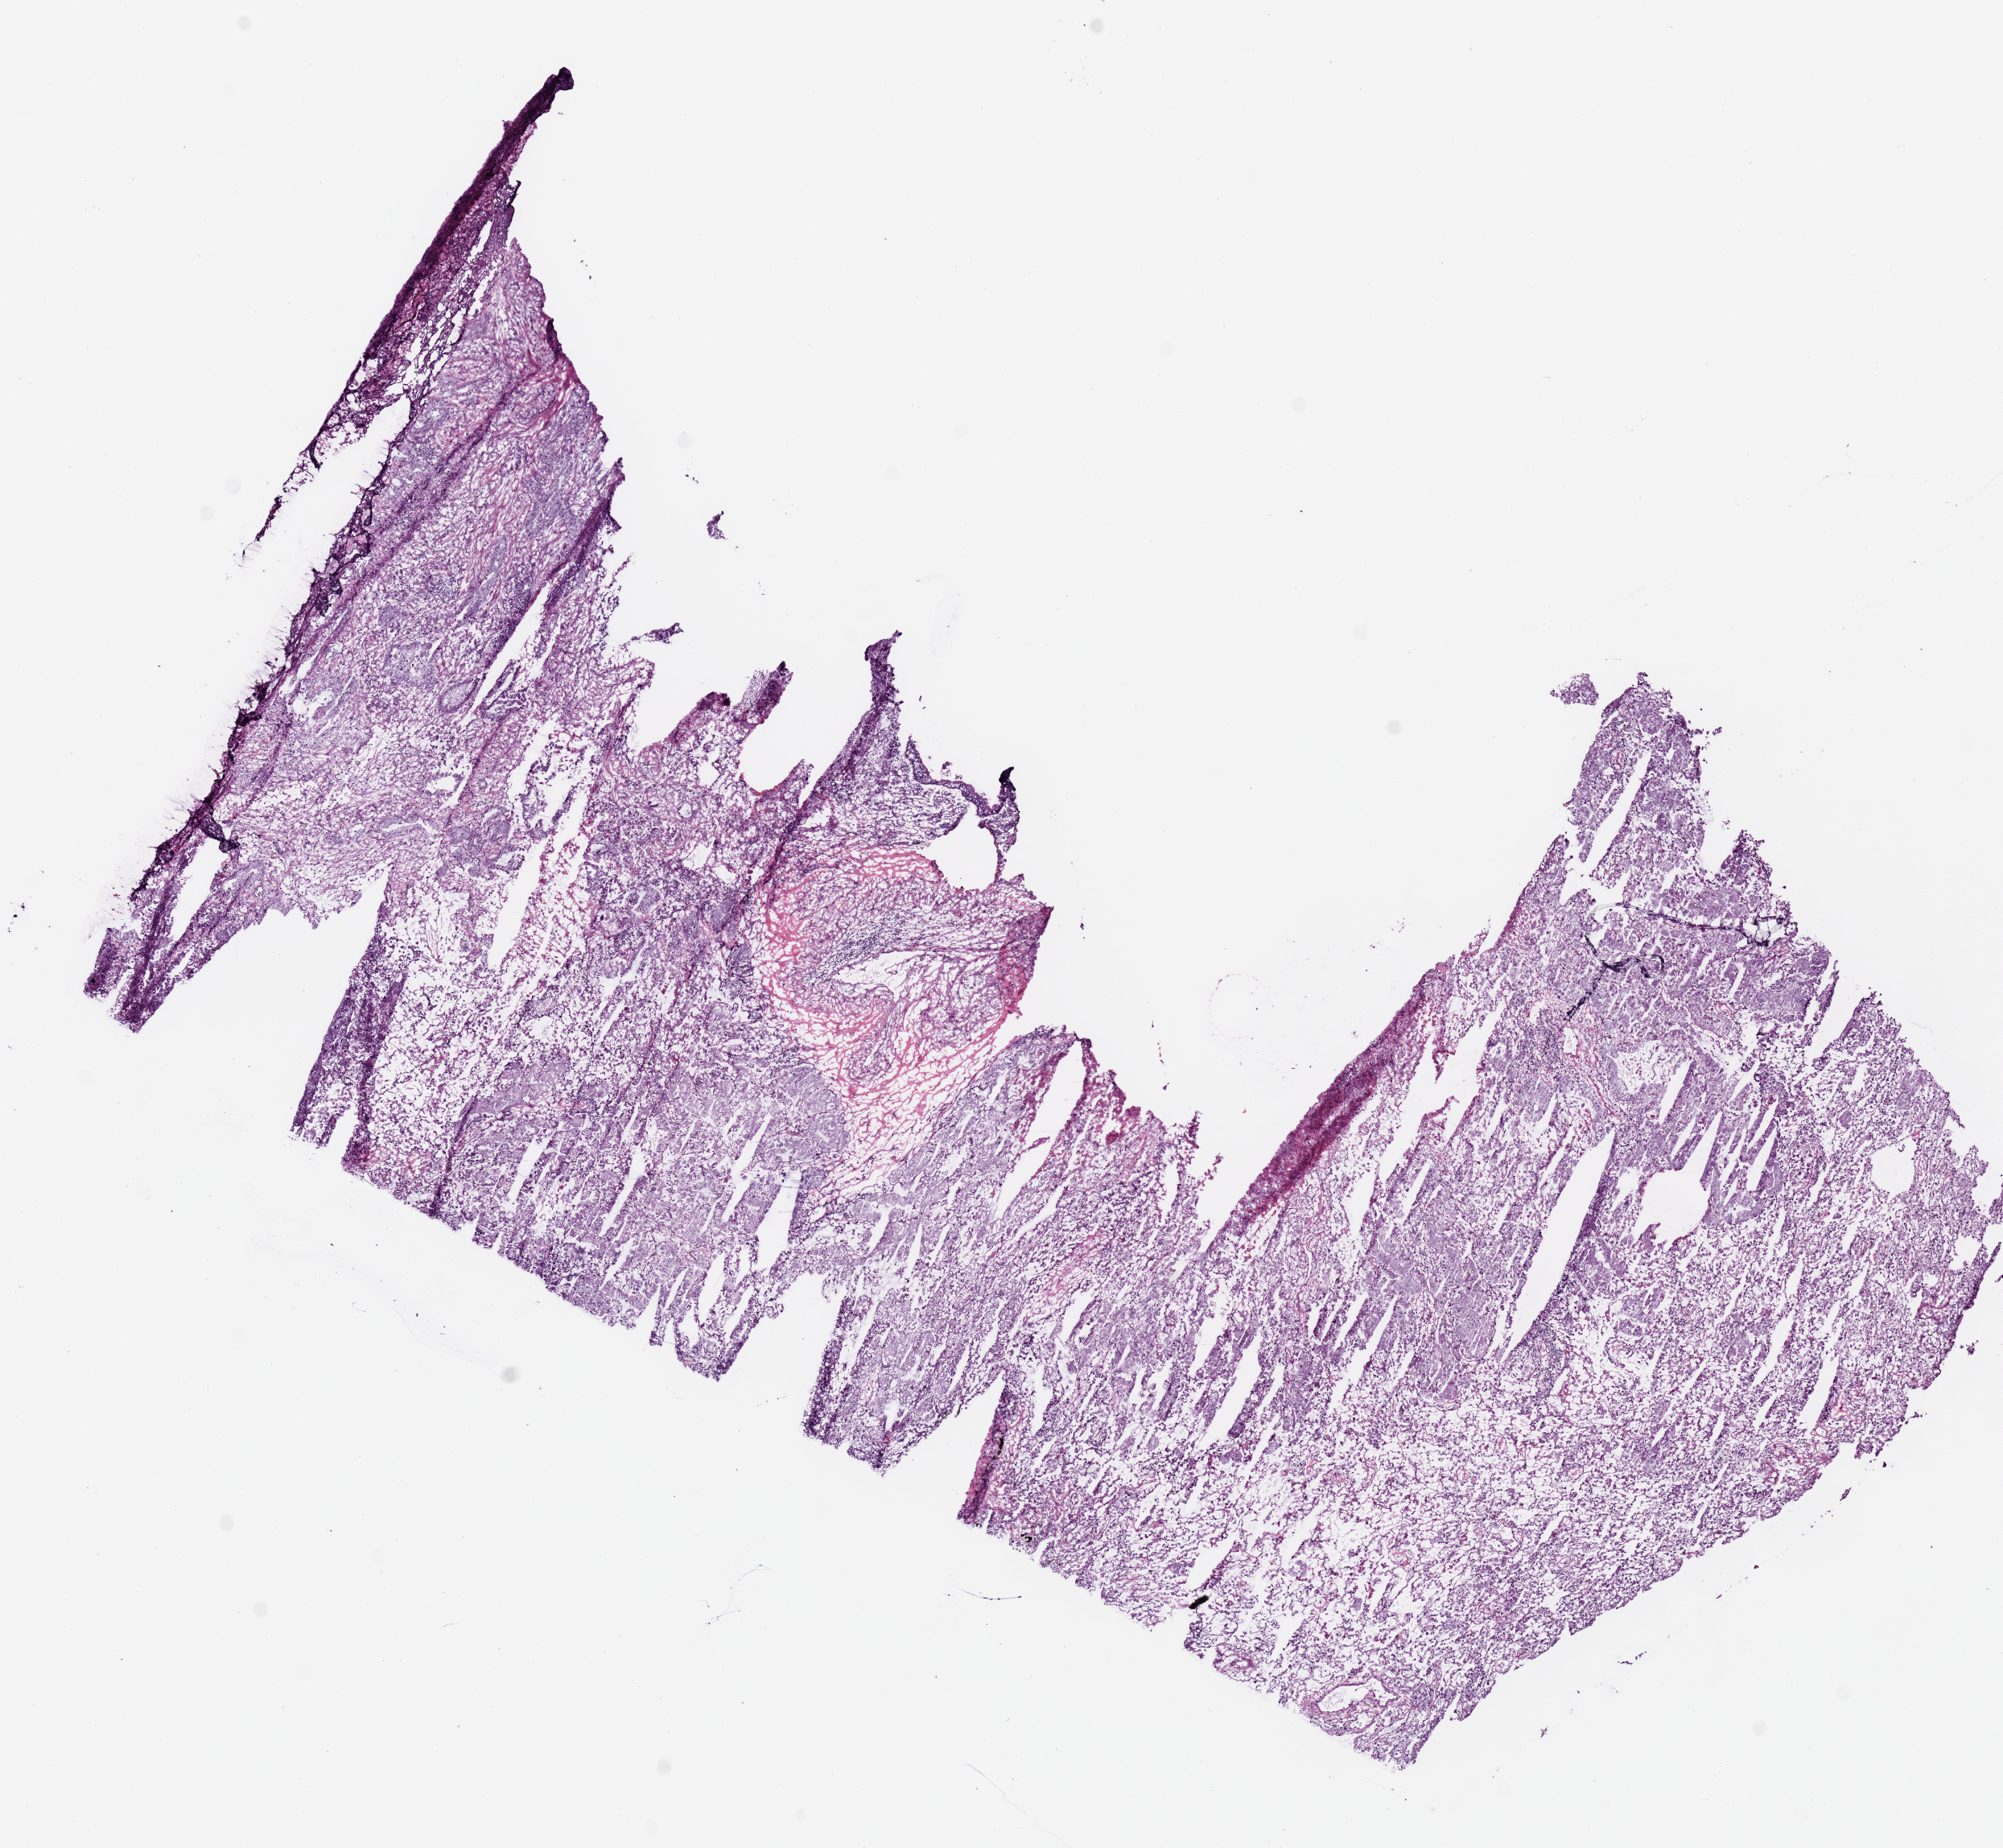
Whole-slide histology image, H&E-stained, shown as a low-resolution overview of the whole scanned area (about 9.8 x 9.1 mm). Frozen section from the top of the tissue portion. Sample: primary tumour, lung. Male patient; age at initial diagnosis 62 years. Pathologist review of this section (percent, as recorded): tumour cells 80%, tumour nuclei 65%, normal cells 18%, stromal cells 0%, necrosis 2%. Inflammatory infiltration, as recorded: lymphocyte infiltration 10%, monocyte infiltration 10%, neutrophil infiltration 10%.
• AJCC pathologic stage: IIIA (7th edition)
• histologic diagnosis: Adenocarcinoma, NOS (lower lobe, lung)
• laterality: right
• TNM: T1a N2 MX